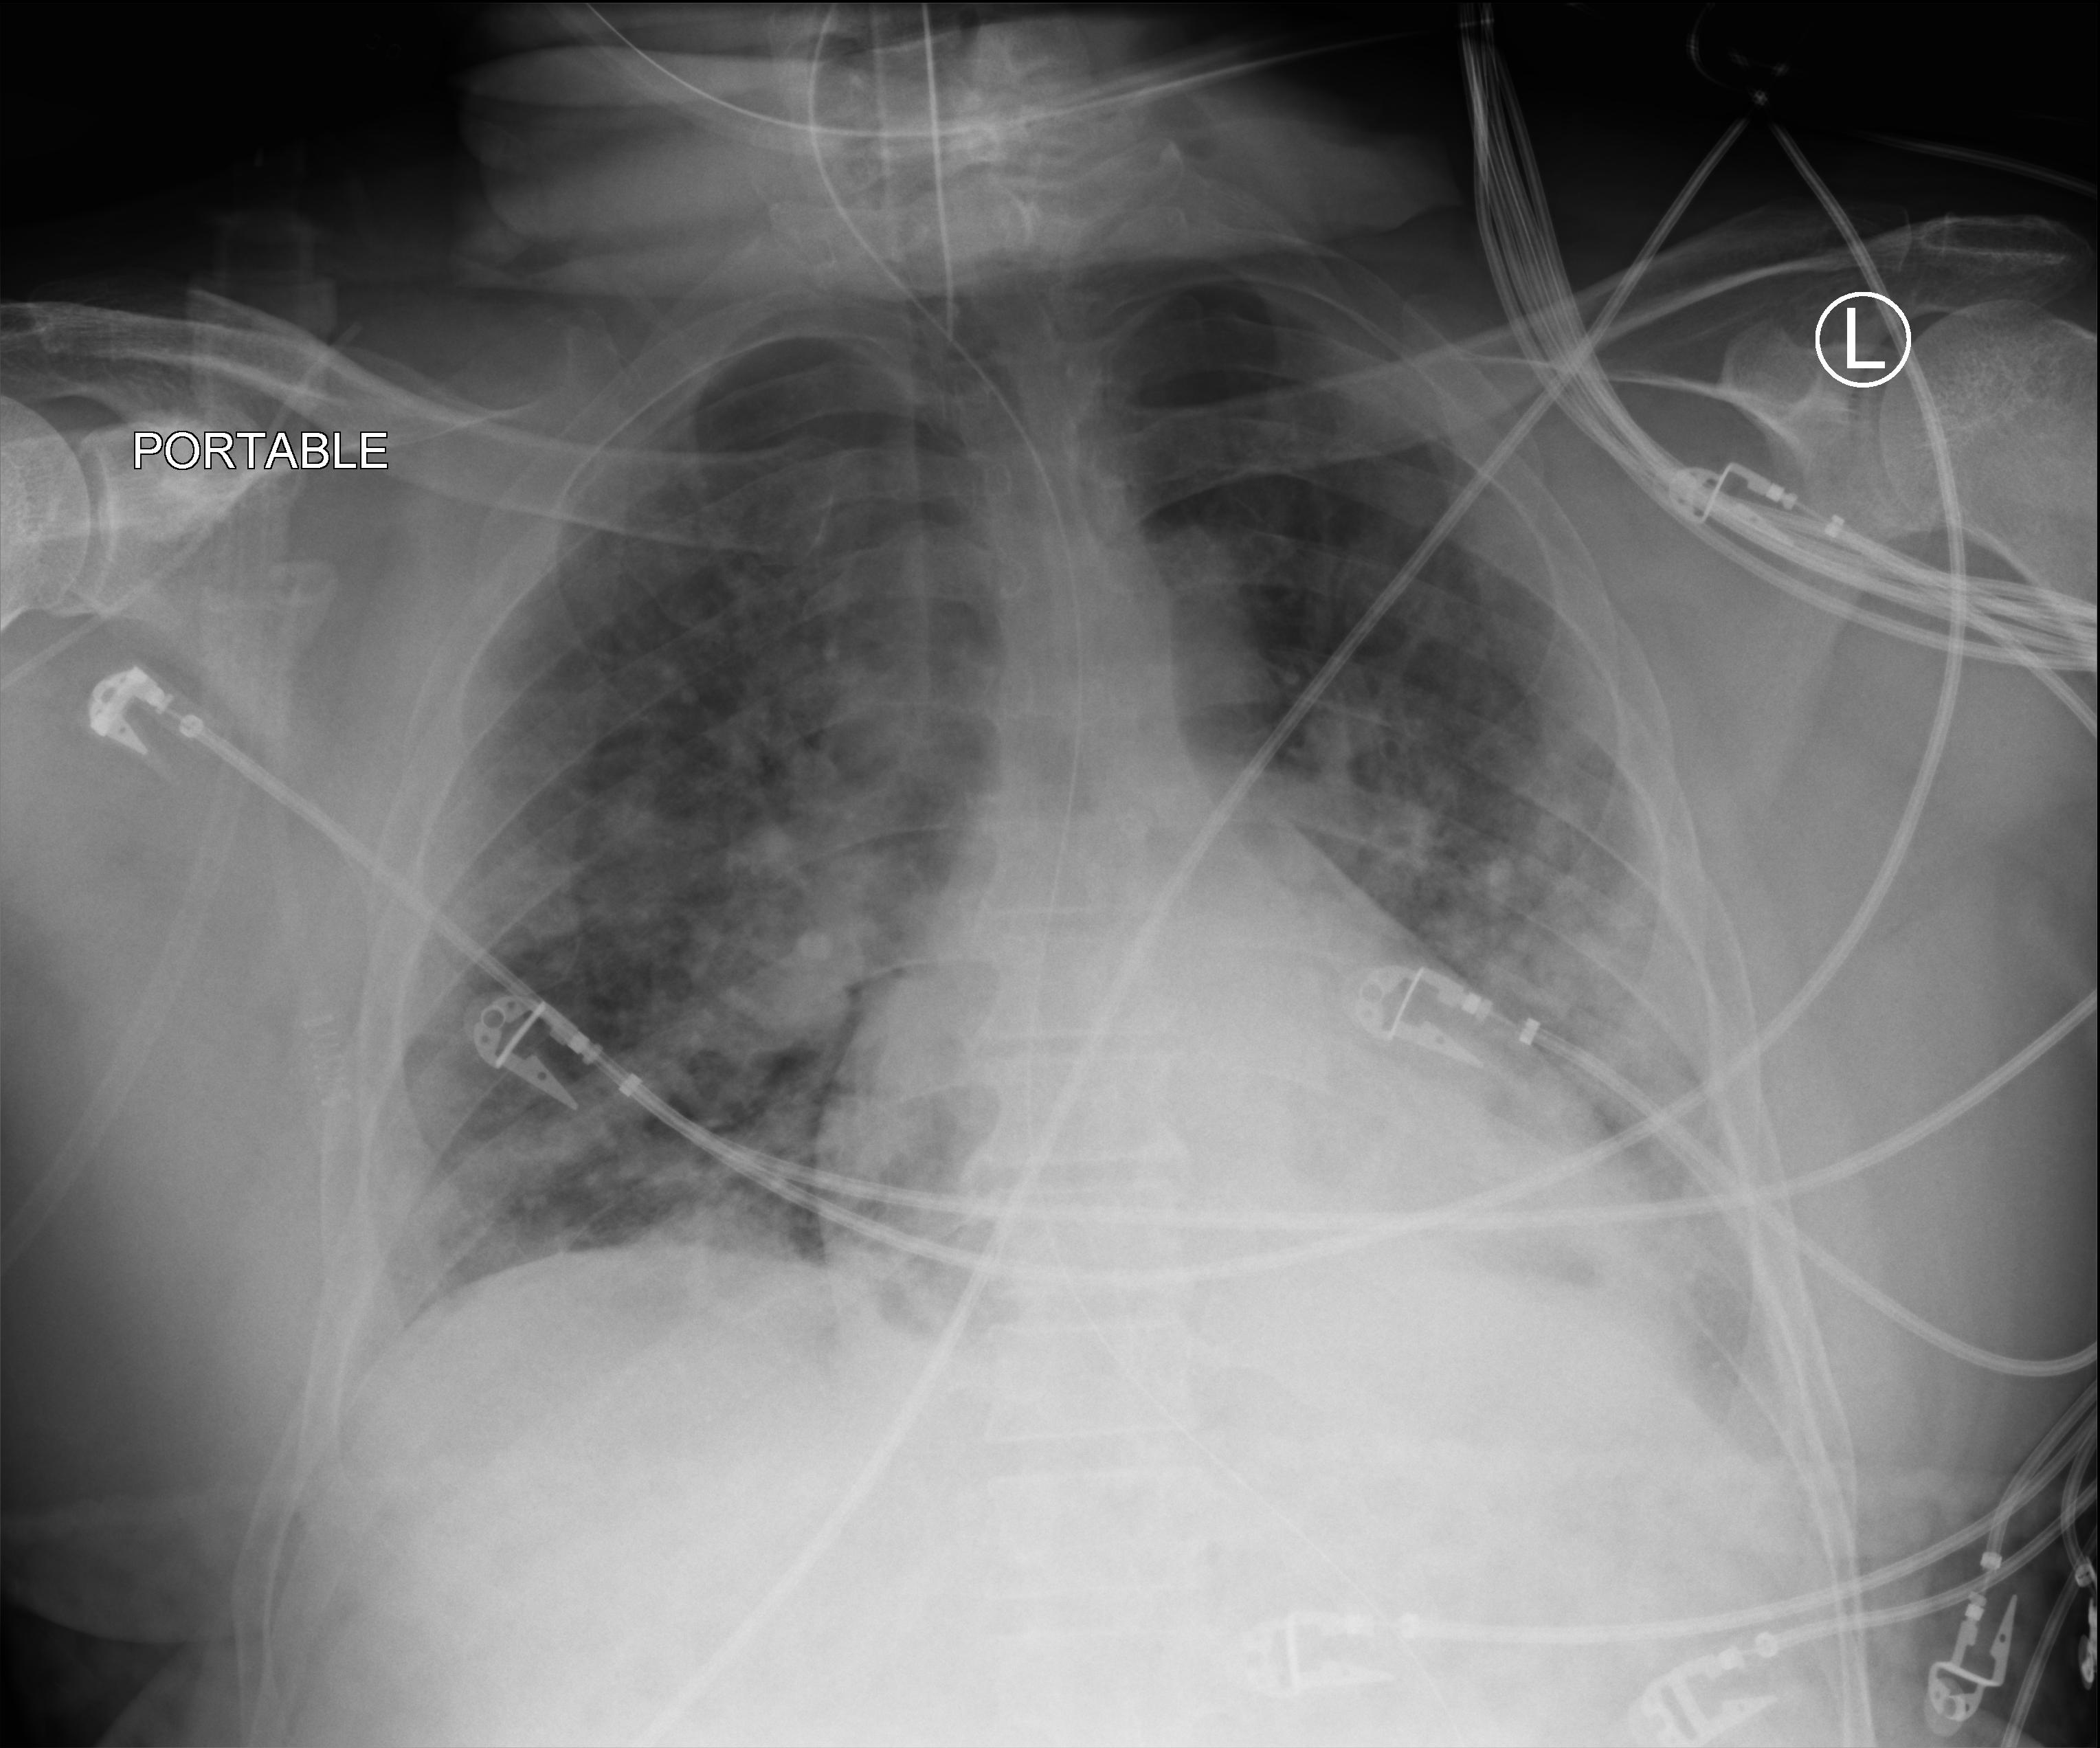
Chest X-ray (portable), anteroposterior (AP) projection. Male patient hospitalised with COVID-19, age 18–59 years.
Admission-level facts for this patient (not findings on this image; timing relative to this image not recorded):
- admitted to intensive care during this hospital stay: yes
- COPD (admission record): yes